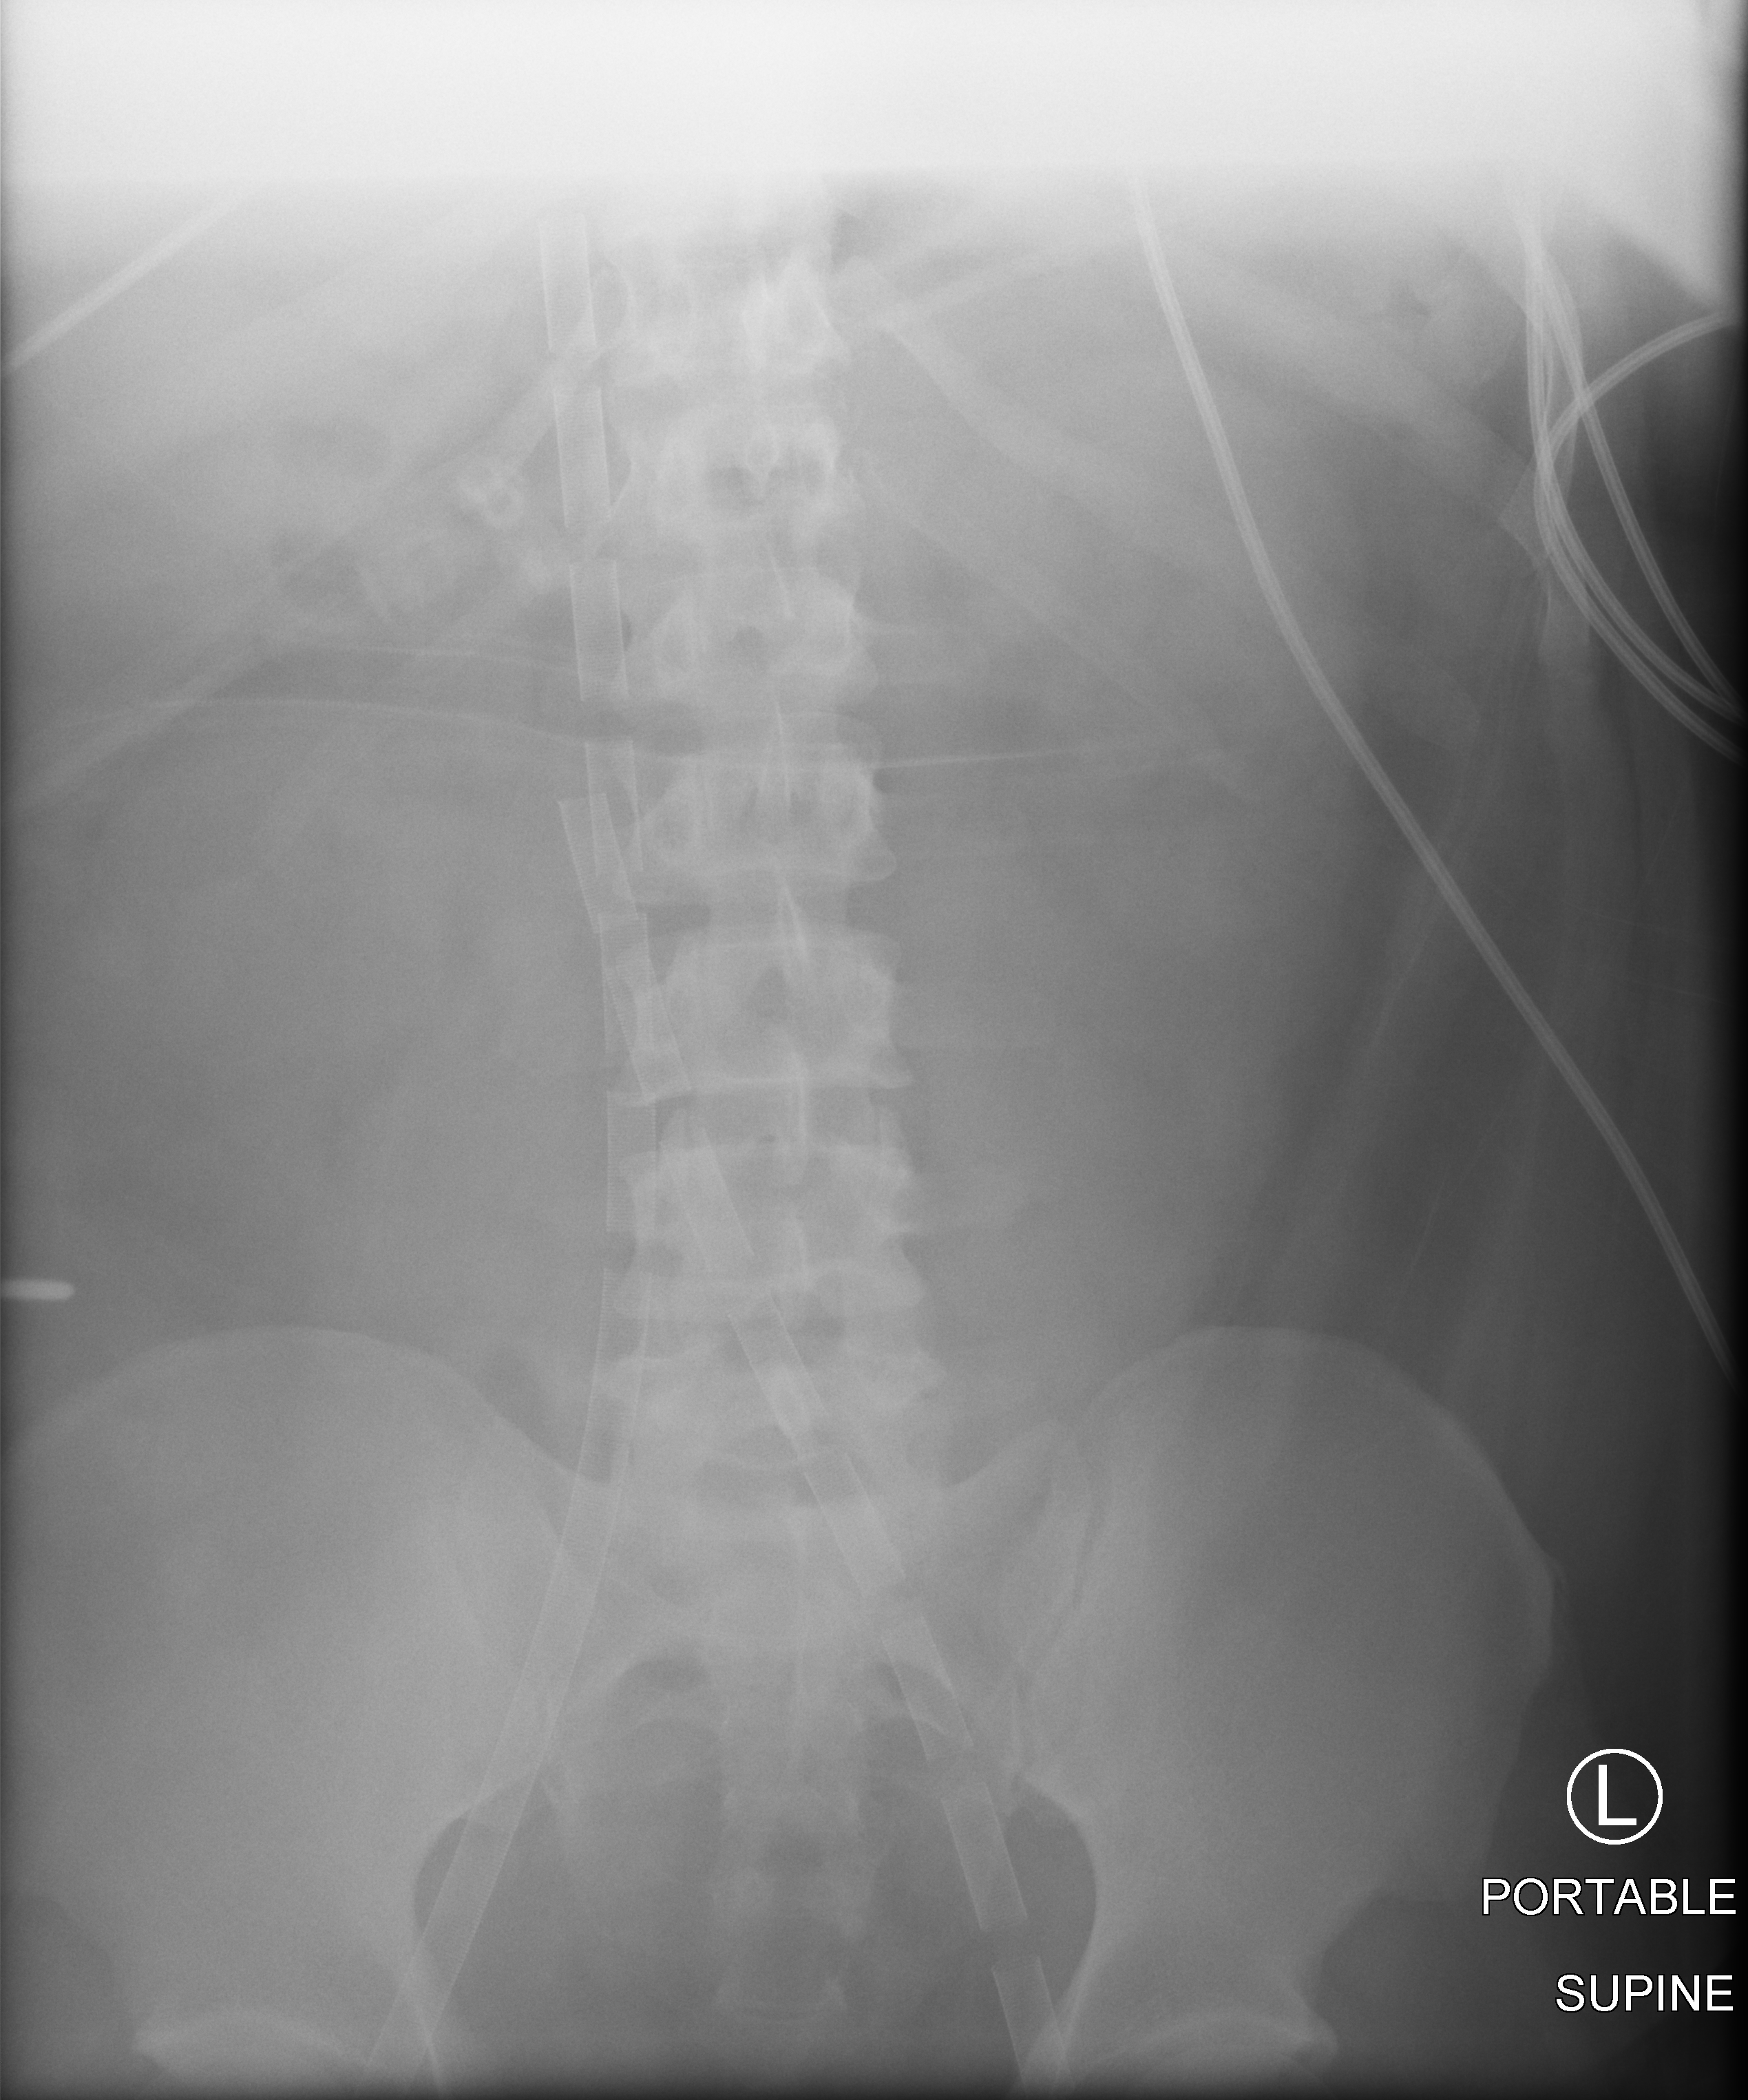
Portable abdomen radiograph; anteroposterior (AP) projection. Patient hospitalised with COVID-19, aged 18–59 years.
Hospital-stay facts (about this admission, not read from this image; timing relative to this image not recorded):
- mechanically ventilated during this hospital stay: yes